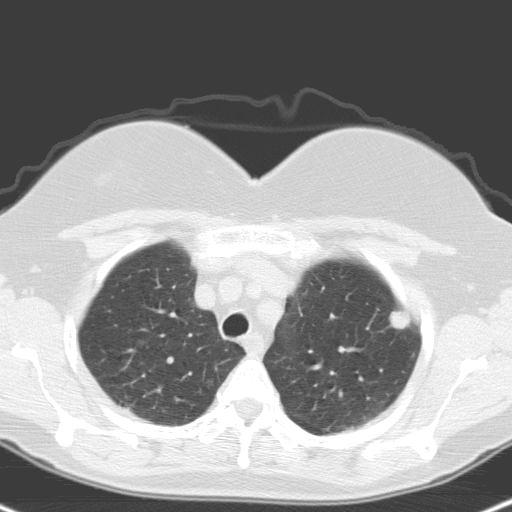
Low-dose screening chest CT, one axial slice; slice 126 of 148 in the series (ordered by position); 120 kVp; lung window (W 1500 / L -600 HU); 3.2 mm slice thickness; 512 × 512 image matrix, field of view 314 × 314 mm.
Annotated regions visible in this slice (outlined manually by an expert reader):
- lesion 1 (tumor, upper lobe of left lung): box from (x=389, y=310) to (x=411, y=330) px